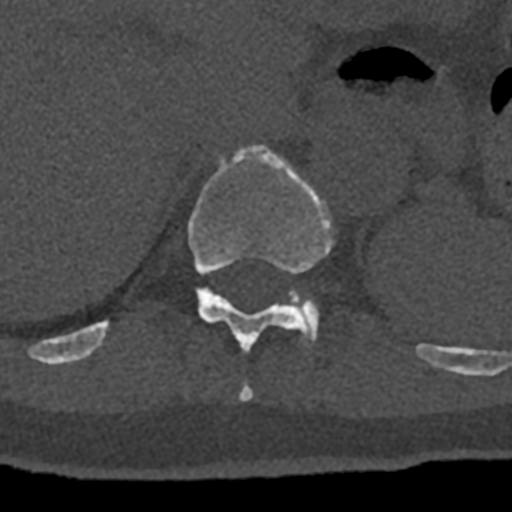
CT including the spine, one axial slice. Reconstruction kernel Br40s/3. 120 kVp. Bone window (W 1800 / L 400 HU). 0.5 mm slice thickness. 512 × 512 image matrix. Male patient, age 74 years. From the clinical record (not read from this slice): primary cancer: renal; vertebrae with lytic lesions (as recorded): T10, L1, L2, L3, L4, L5.
Structures marked on this image (semi-automatically segmented with operator editing):
- T10 vertebra: bounding box (x1, y1, x2, y2) in pixels: (239, 384, 254, 401)
- T11 vertebra: (70, 144, 432, 365)
- T12 vertebra: (289, 290, 319, 340)